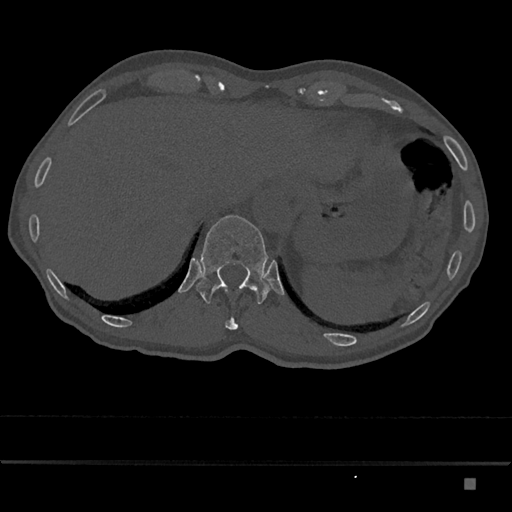
CT including the spine, one axial slice. Slice 629 of 797 in the series (ordered by position). 120 kVp. Bone window (W 1800 / L 400 HU). 512 × 512 image matrix, field of view 390 × 390 mm. Male patient, age 72 years. From the clinical record (not read from this slice): primary cancer: prostate.
Outlined on this slice (semi-automatically segmented with operator editing):
- T11 vertebra: bounding box <225,317,238,330> (left, top, right, bottom; pixels)
- T12 vertebra: <196,215,270,304>